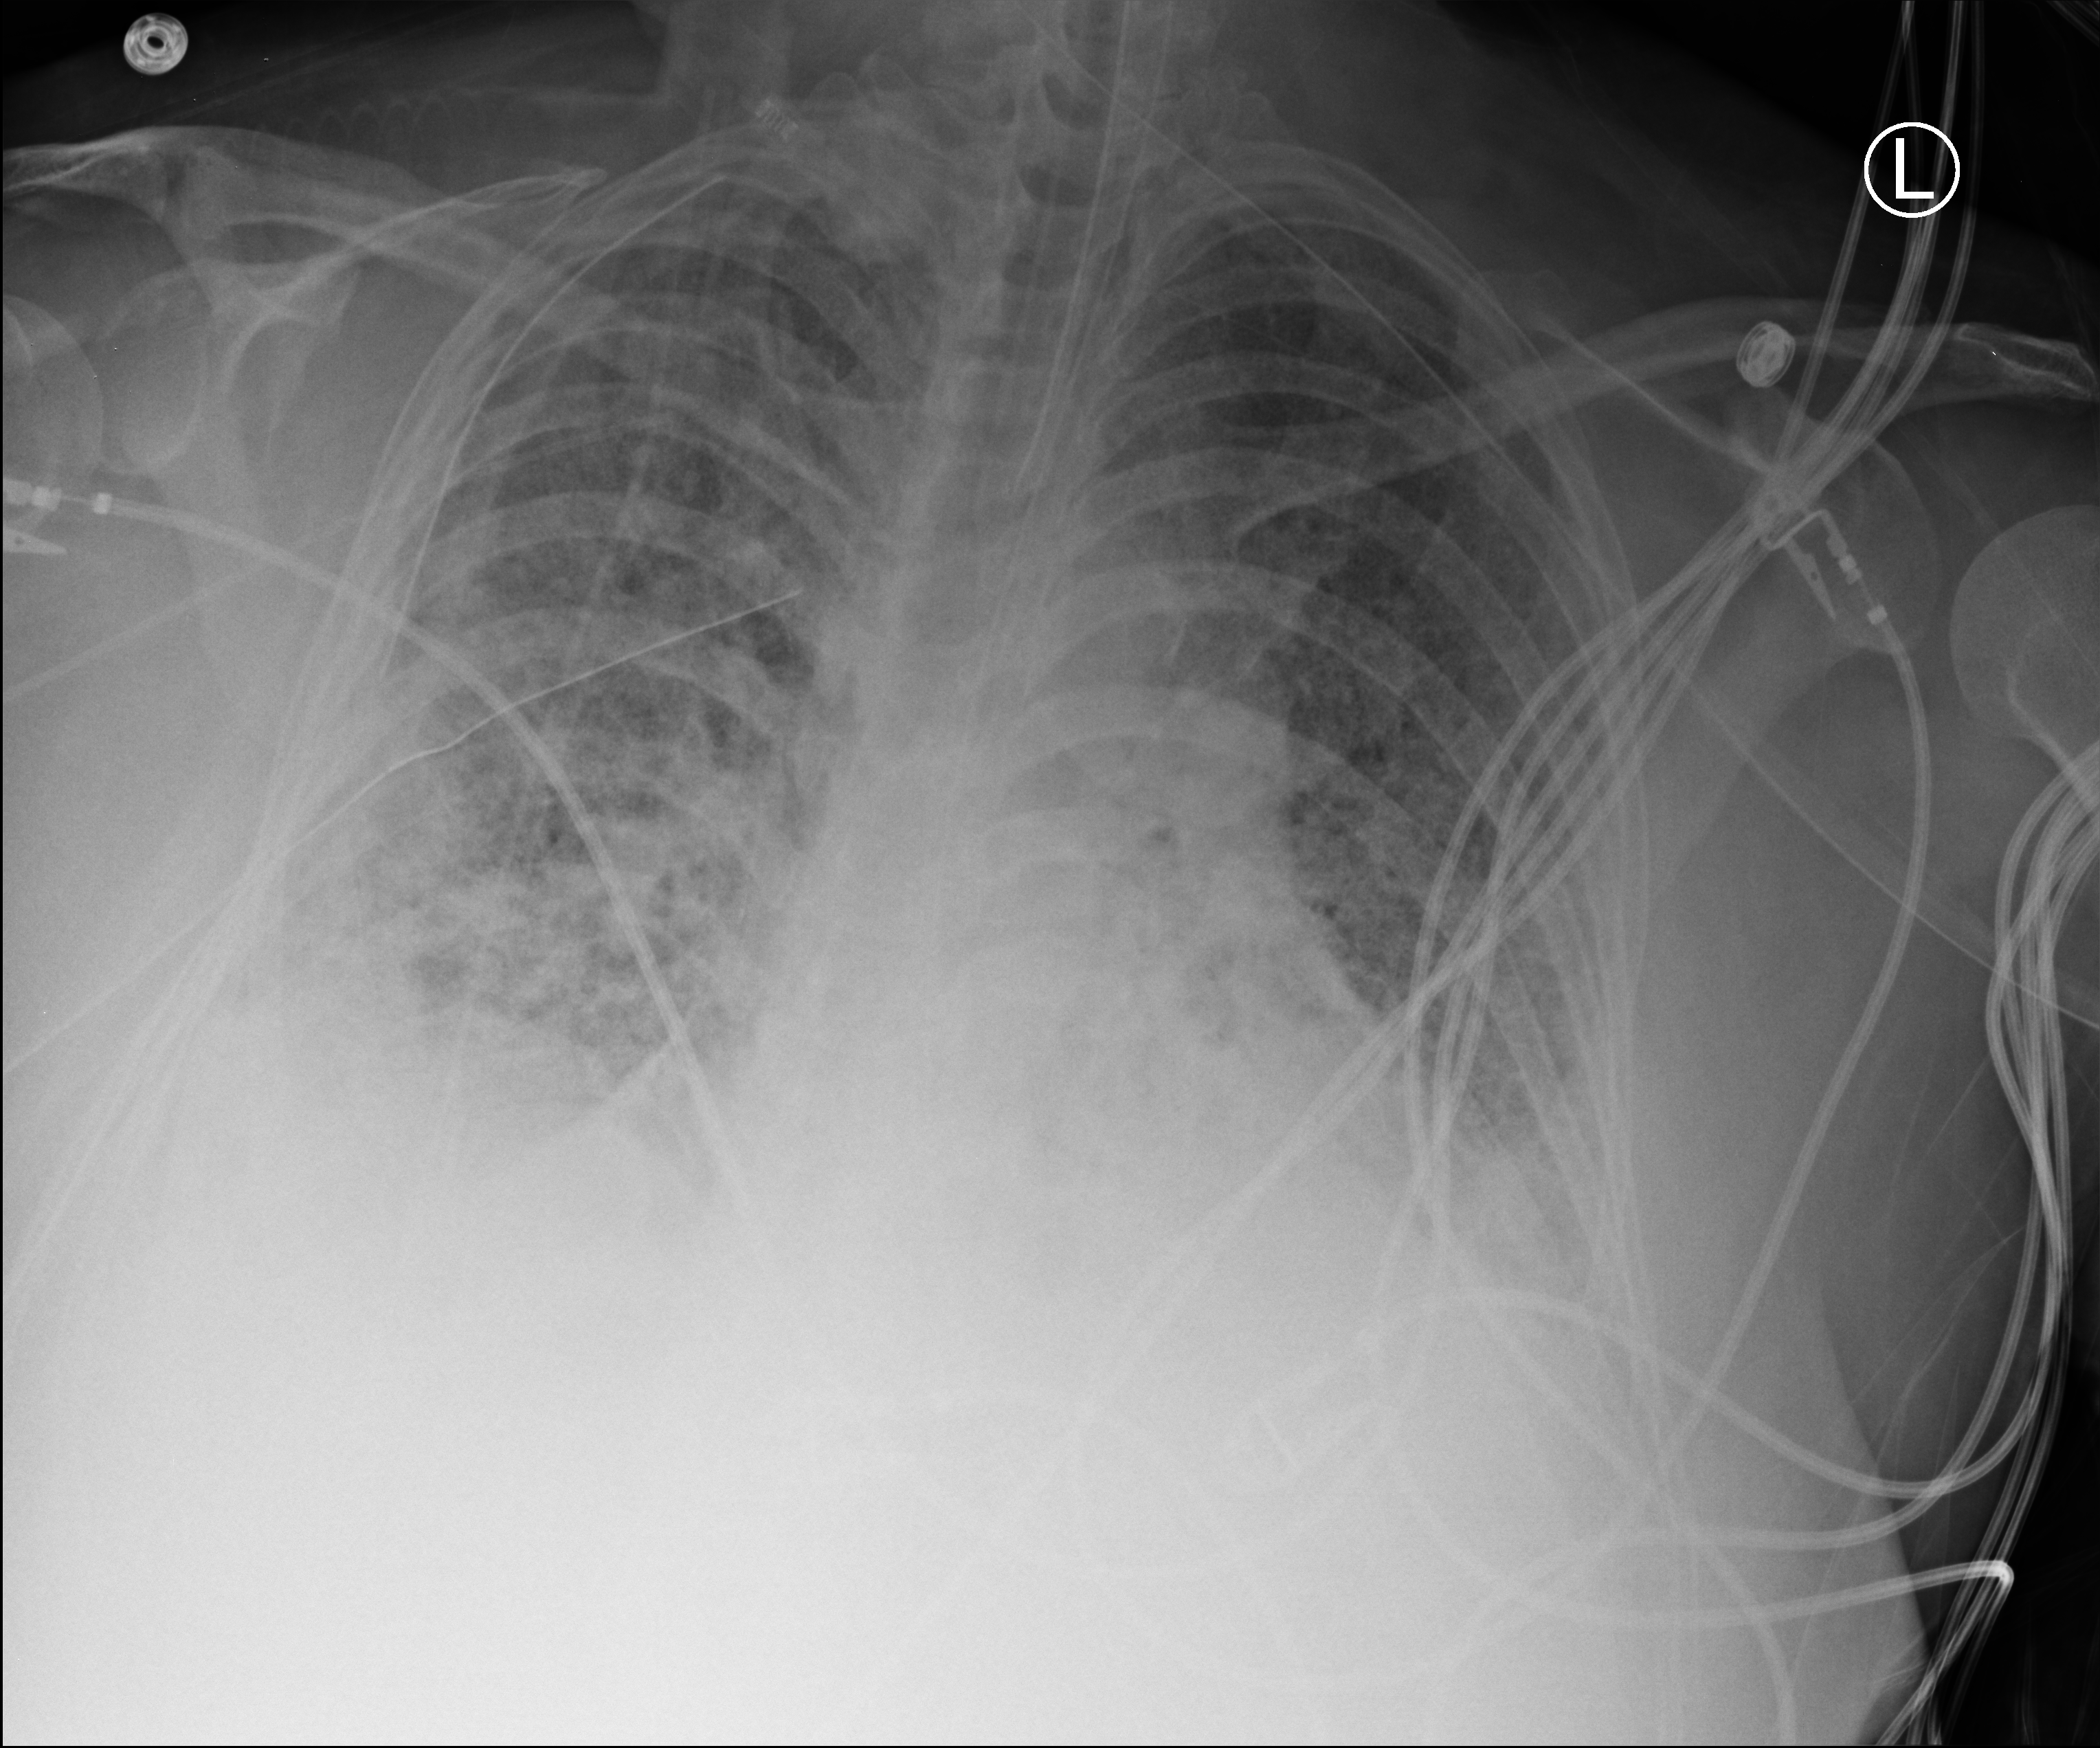
Chest X-ray (portable), anteroposterior (AP) projection. Patient hospitalised with COVID-19, aged 18–59 years.
Hospital-stay facts (about this admission, not read from this image; timing relative to this image not recorded): COPD (admission record): no.